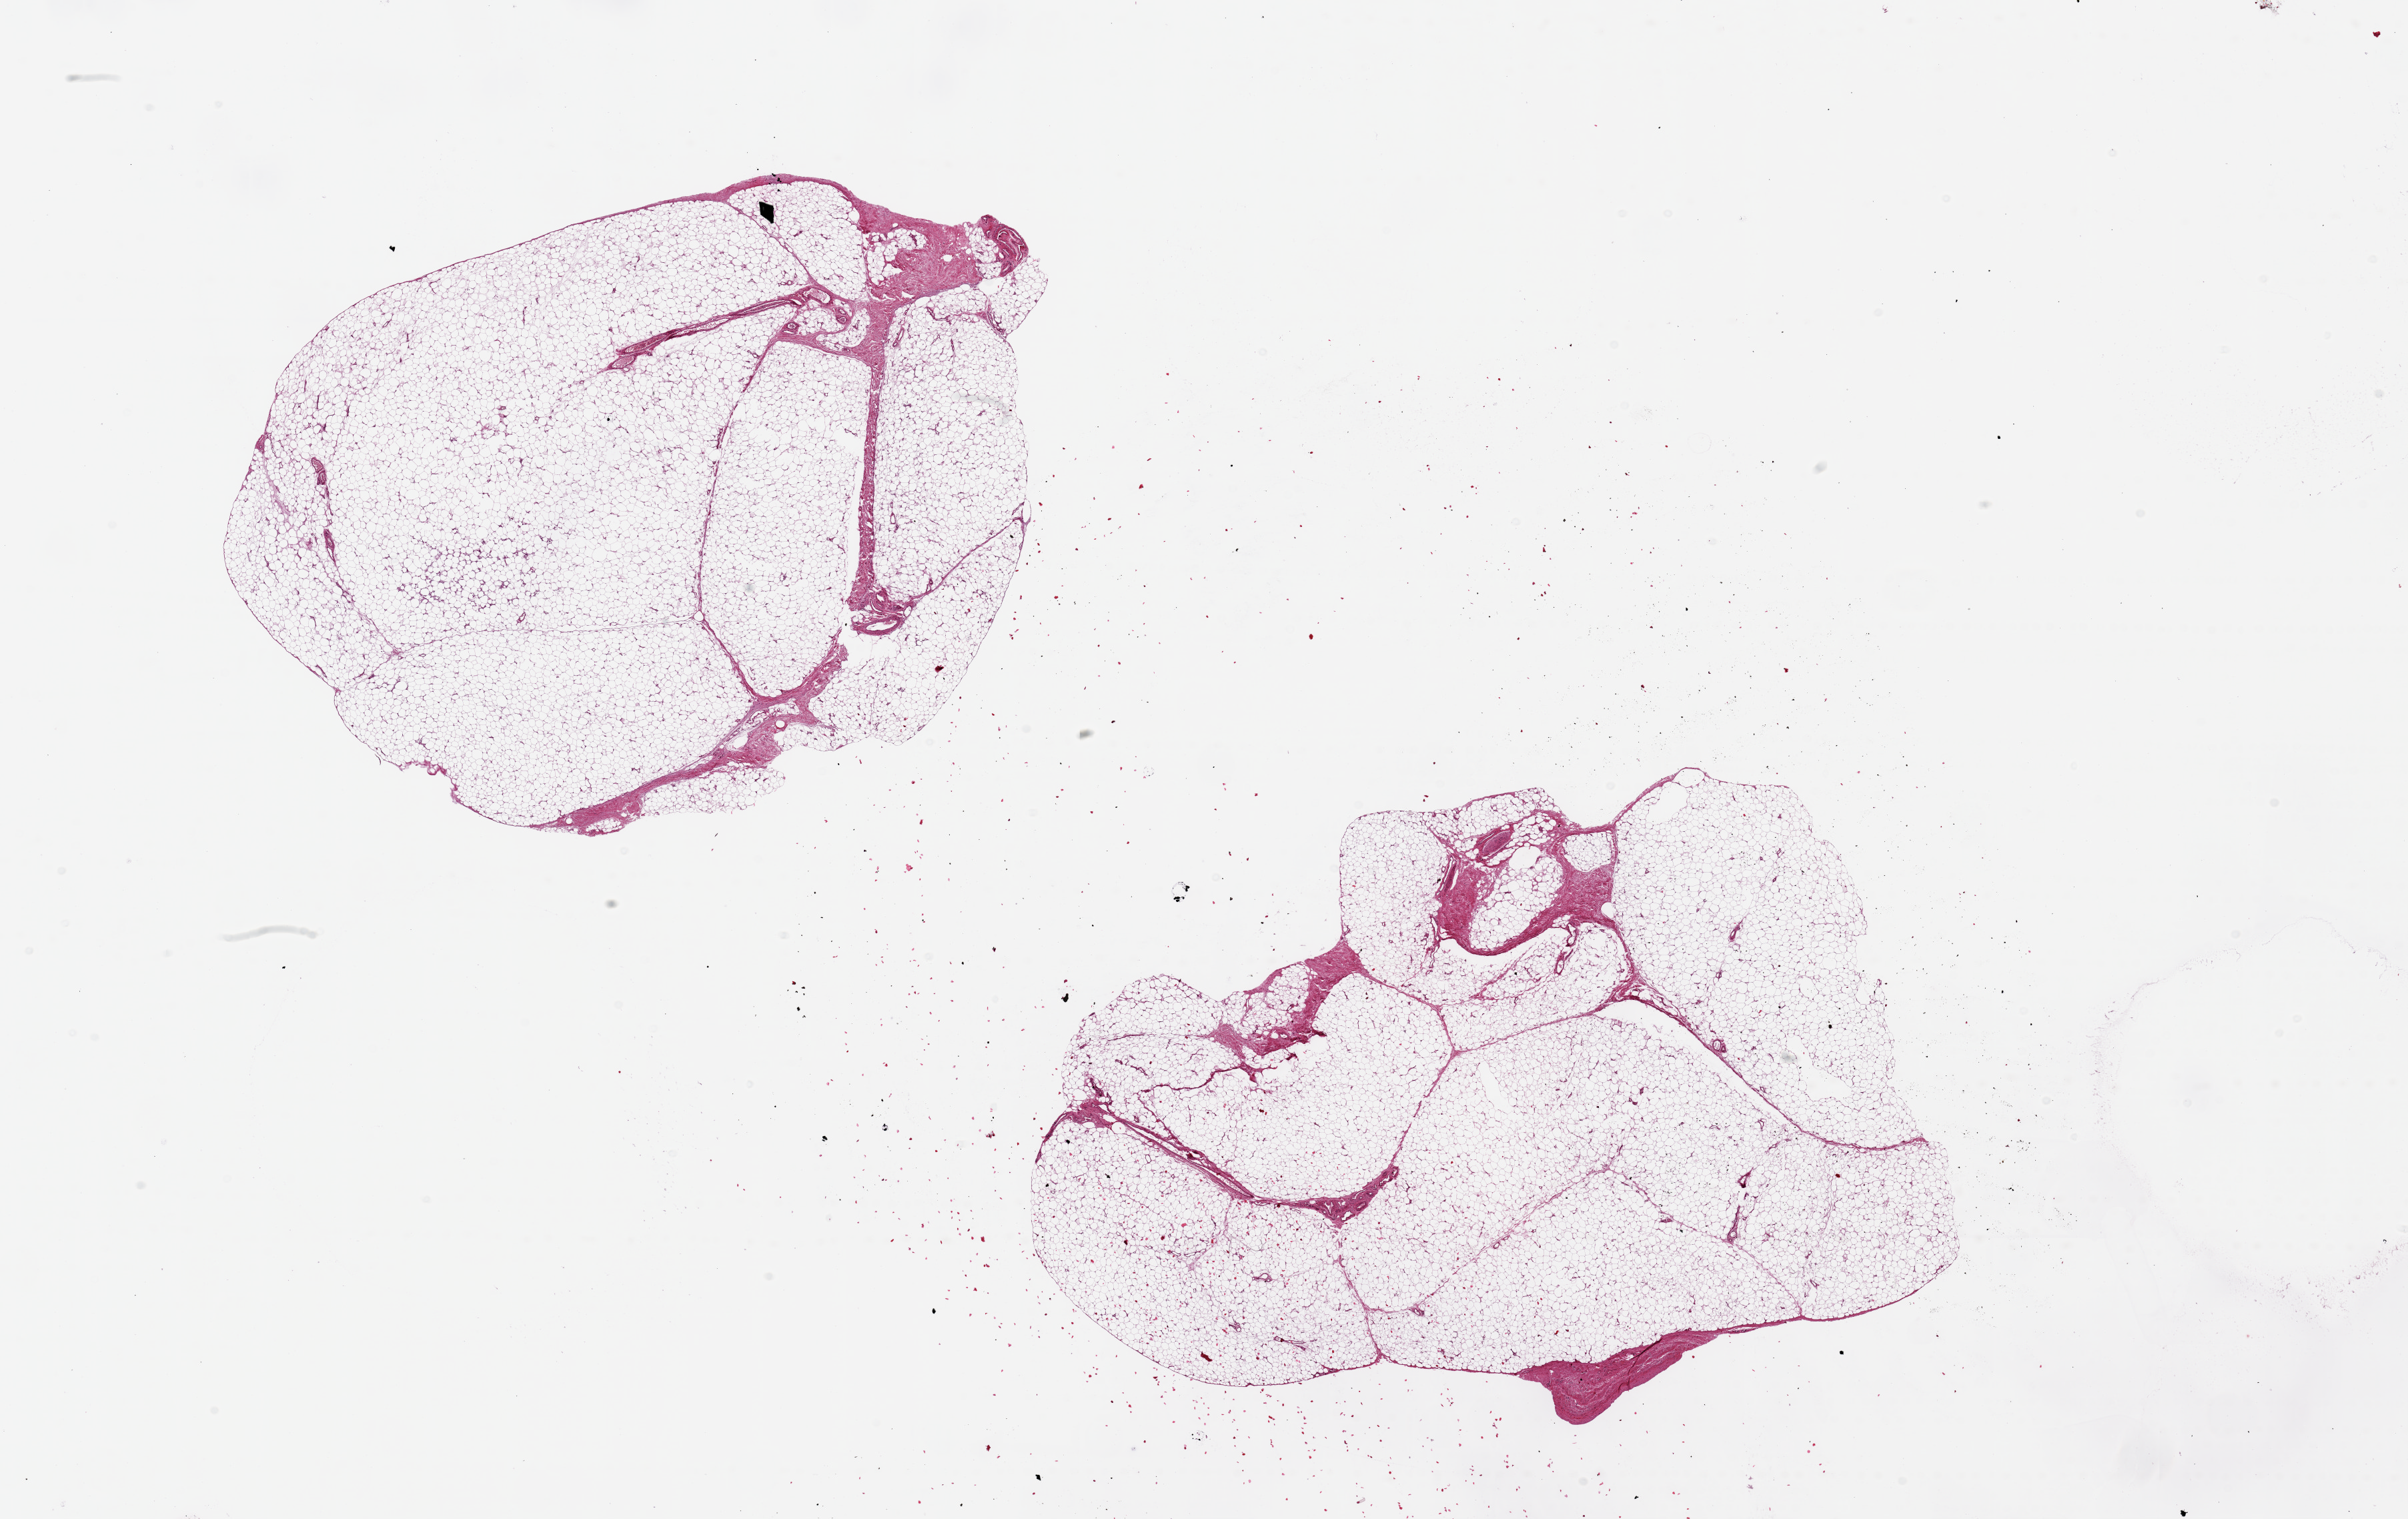
H&E whole-slide image, low-resolution overview of the scanned area, about 28.5 x 18.0 mm (slide scanned at 20x), PAXgene-fixed paraffin-embedded (PFPE) section, sampled site (target tissue): adipose tissue, tissue donor sample. Male donor.
• reviewer comment on this tissue sample: 2 pieces ~9x7mm